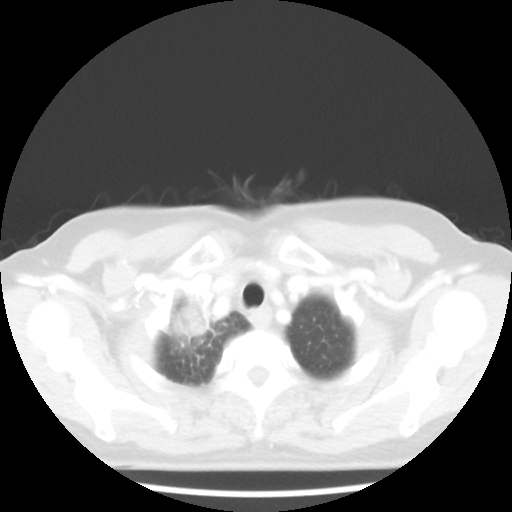
Chest CT, one axial slice; slice 40 of 44 in the series (ordered by position); 100 kVp; lung window (W 1500 / L -600 HU); 5 mm slice thickness; 512 × 512 image matrix. Female patient, age 62 years. From the clinical record (not read from this slice): clinical TNM (as recorded): T3 N0 M0; histopathological grade: G3.
Outlined on this slice (rectangle marked by the reading radiologist):
- lung tumour (recorded histology: small cell carcinoma): box from (x=165, y=294) to (x=227, y=342) px